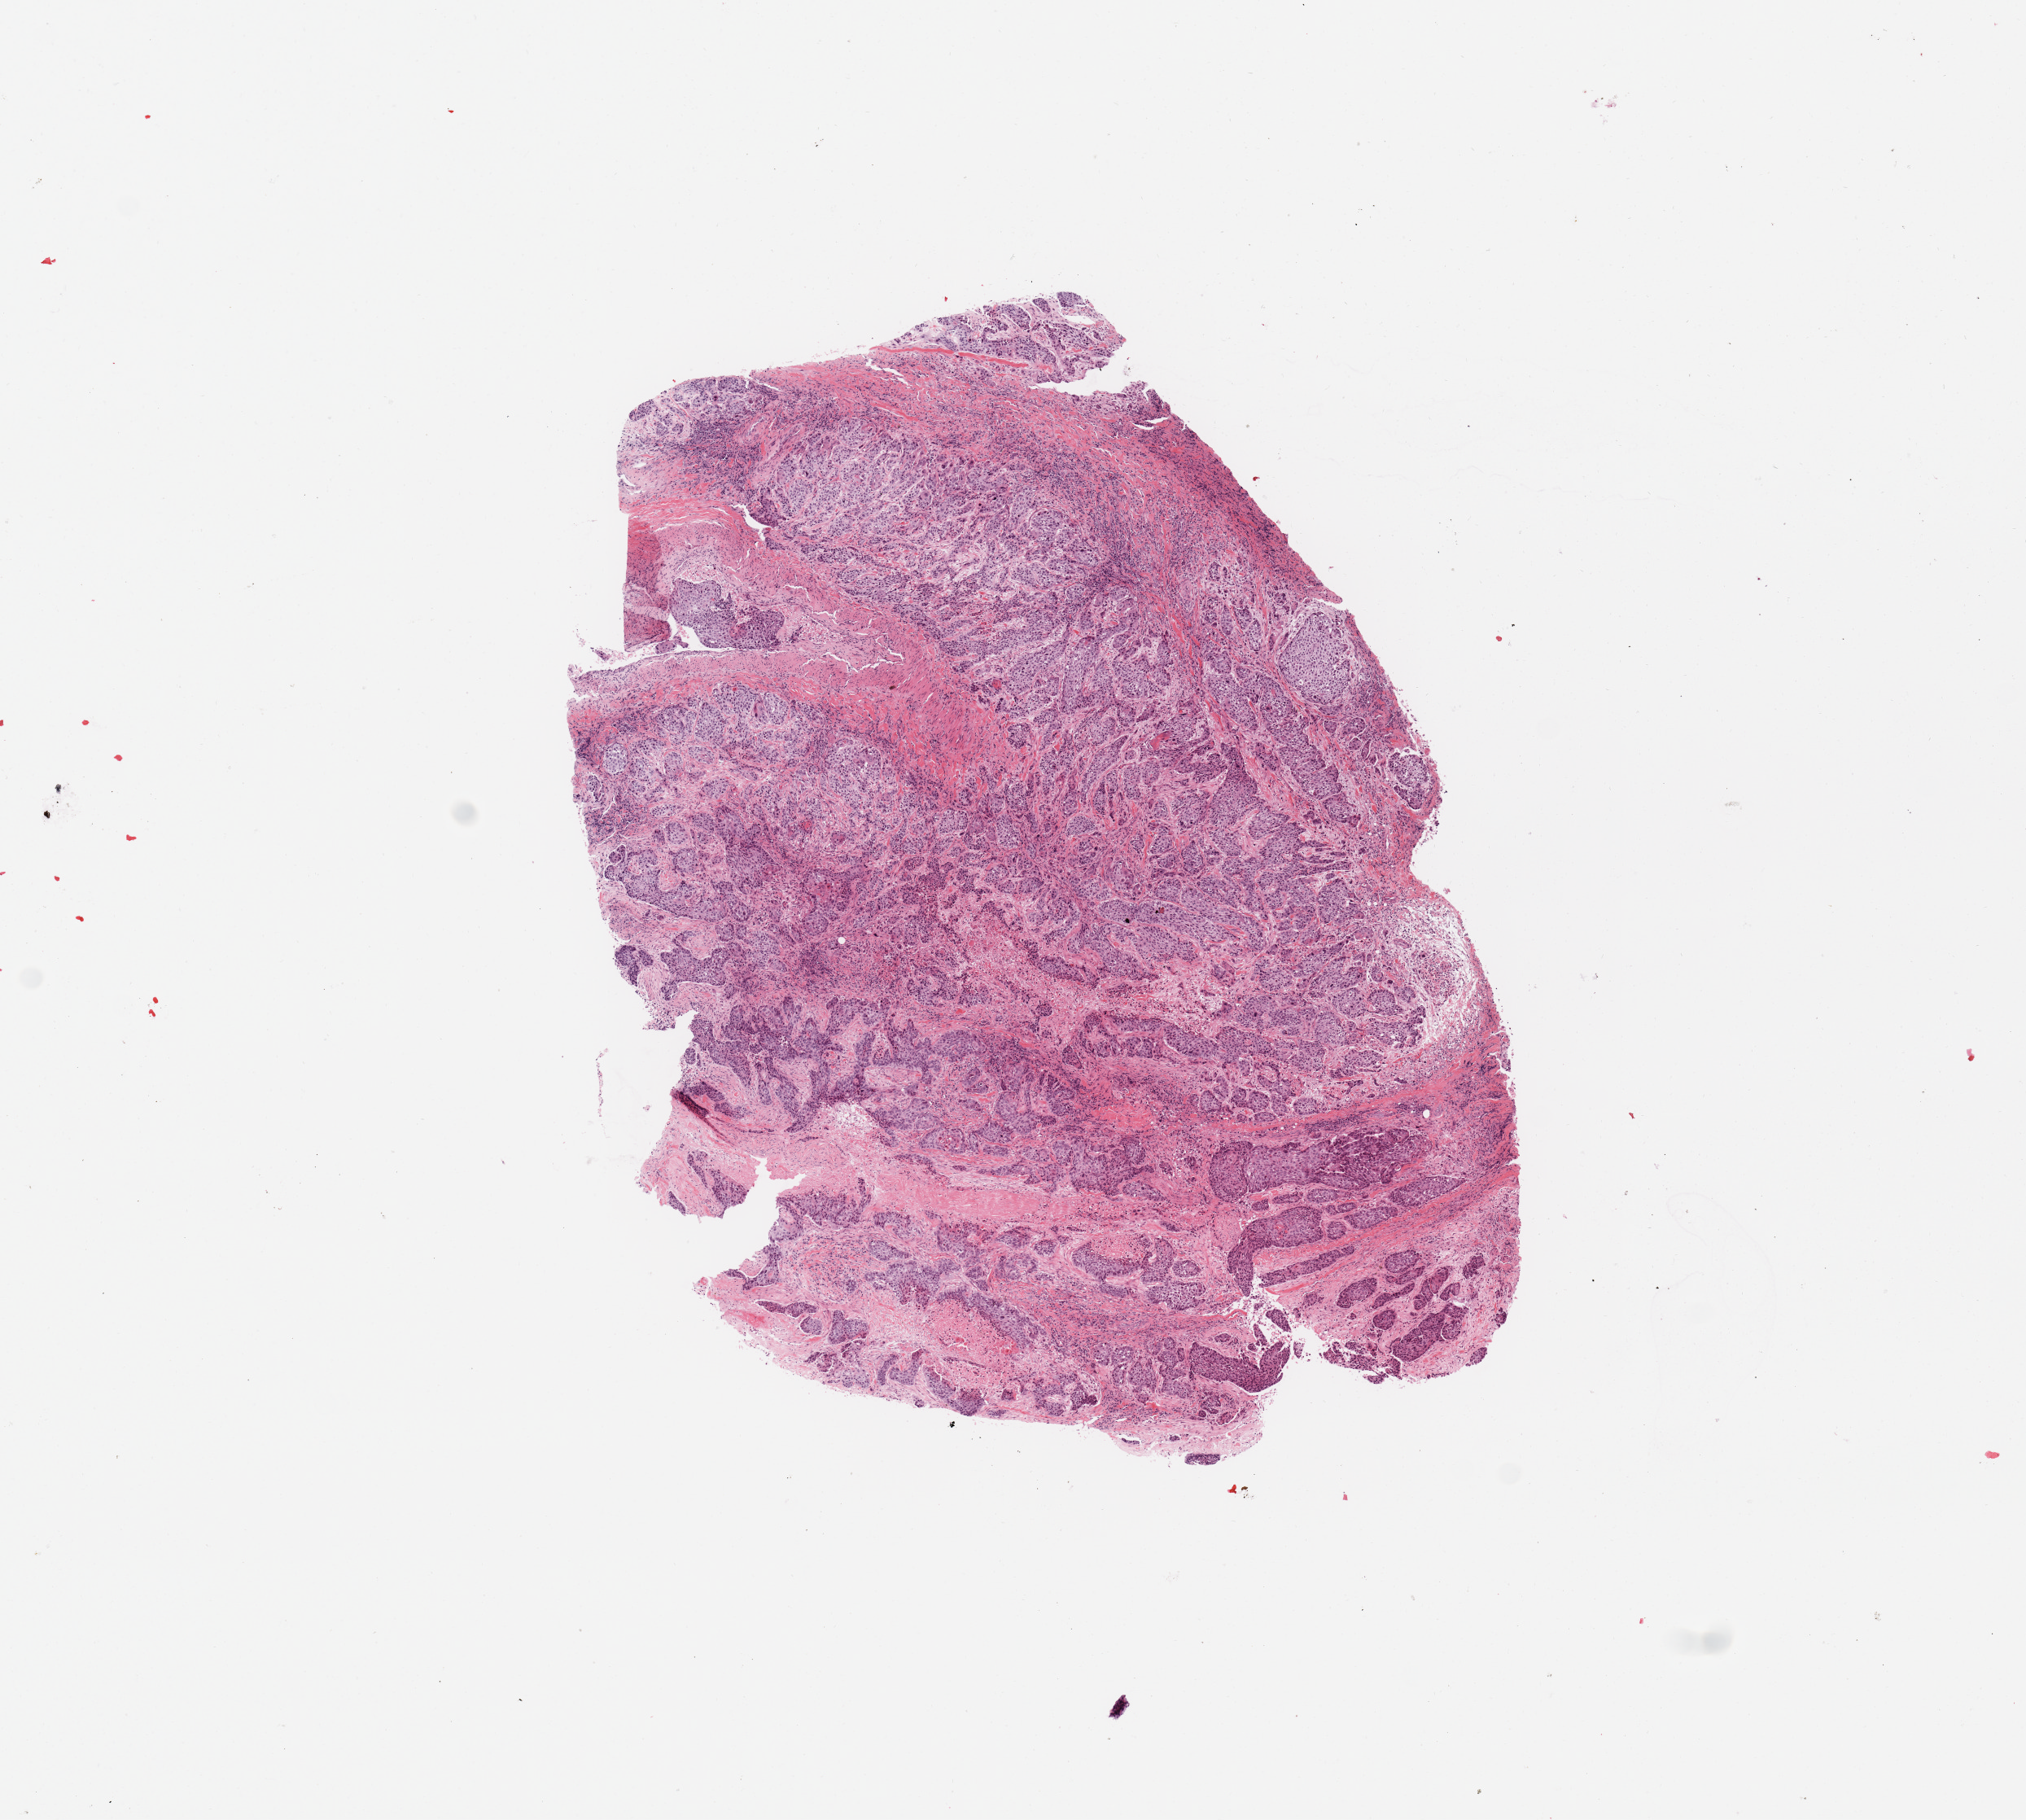
Digitized H&E-stained tissue section (whole slide) — low-resolution overview of the scanned area, about 9.8 x 8.8 mm (slide scanned at 20x). Tumour tissue sample, sampled site: lung. Patient: male, age 62 years. Histologic grade: G3 (poorly differentiated). Composition of this section per pathologist review: tumour nuclei 80%, necrosis 2%.
Primary tumour site (as recorded): right upper lobe. AJCC pathologic stage: IIIA. Diagnosis: Squamous cell carcinoma, NOS.